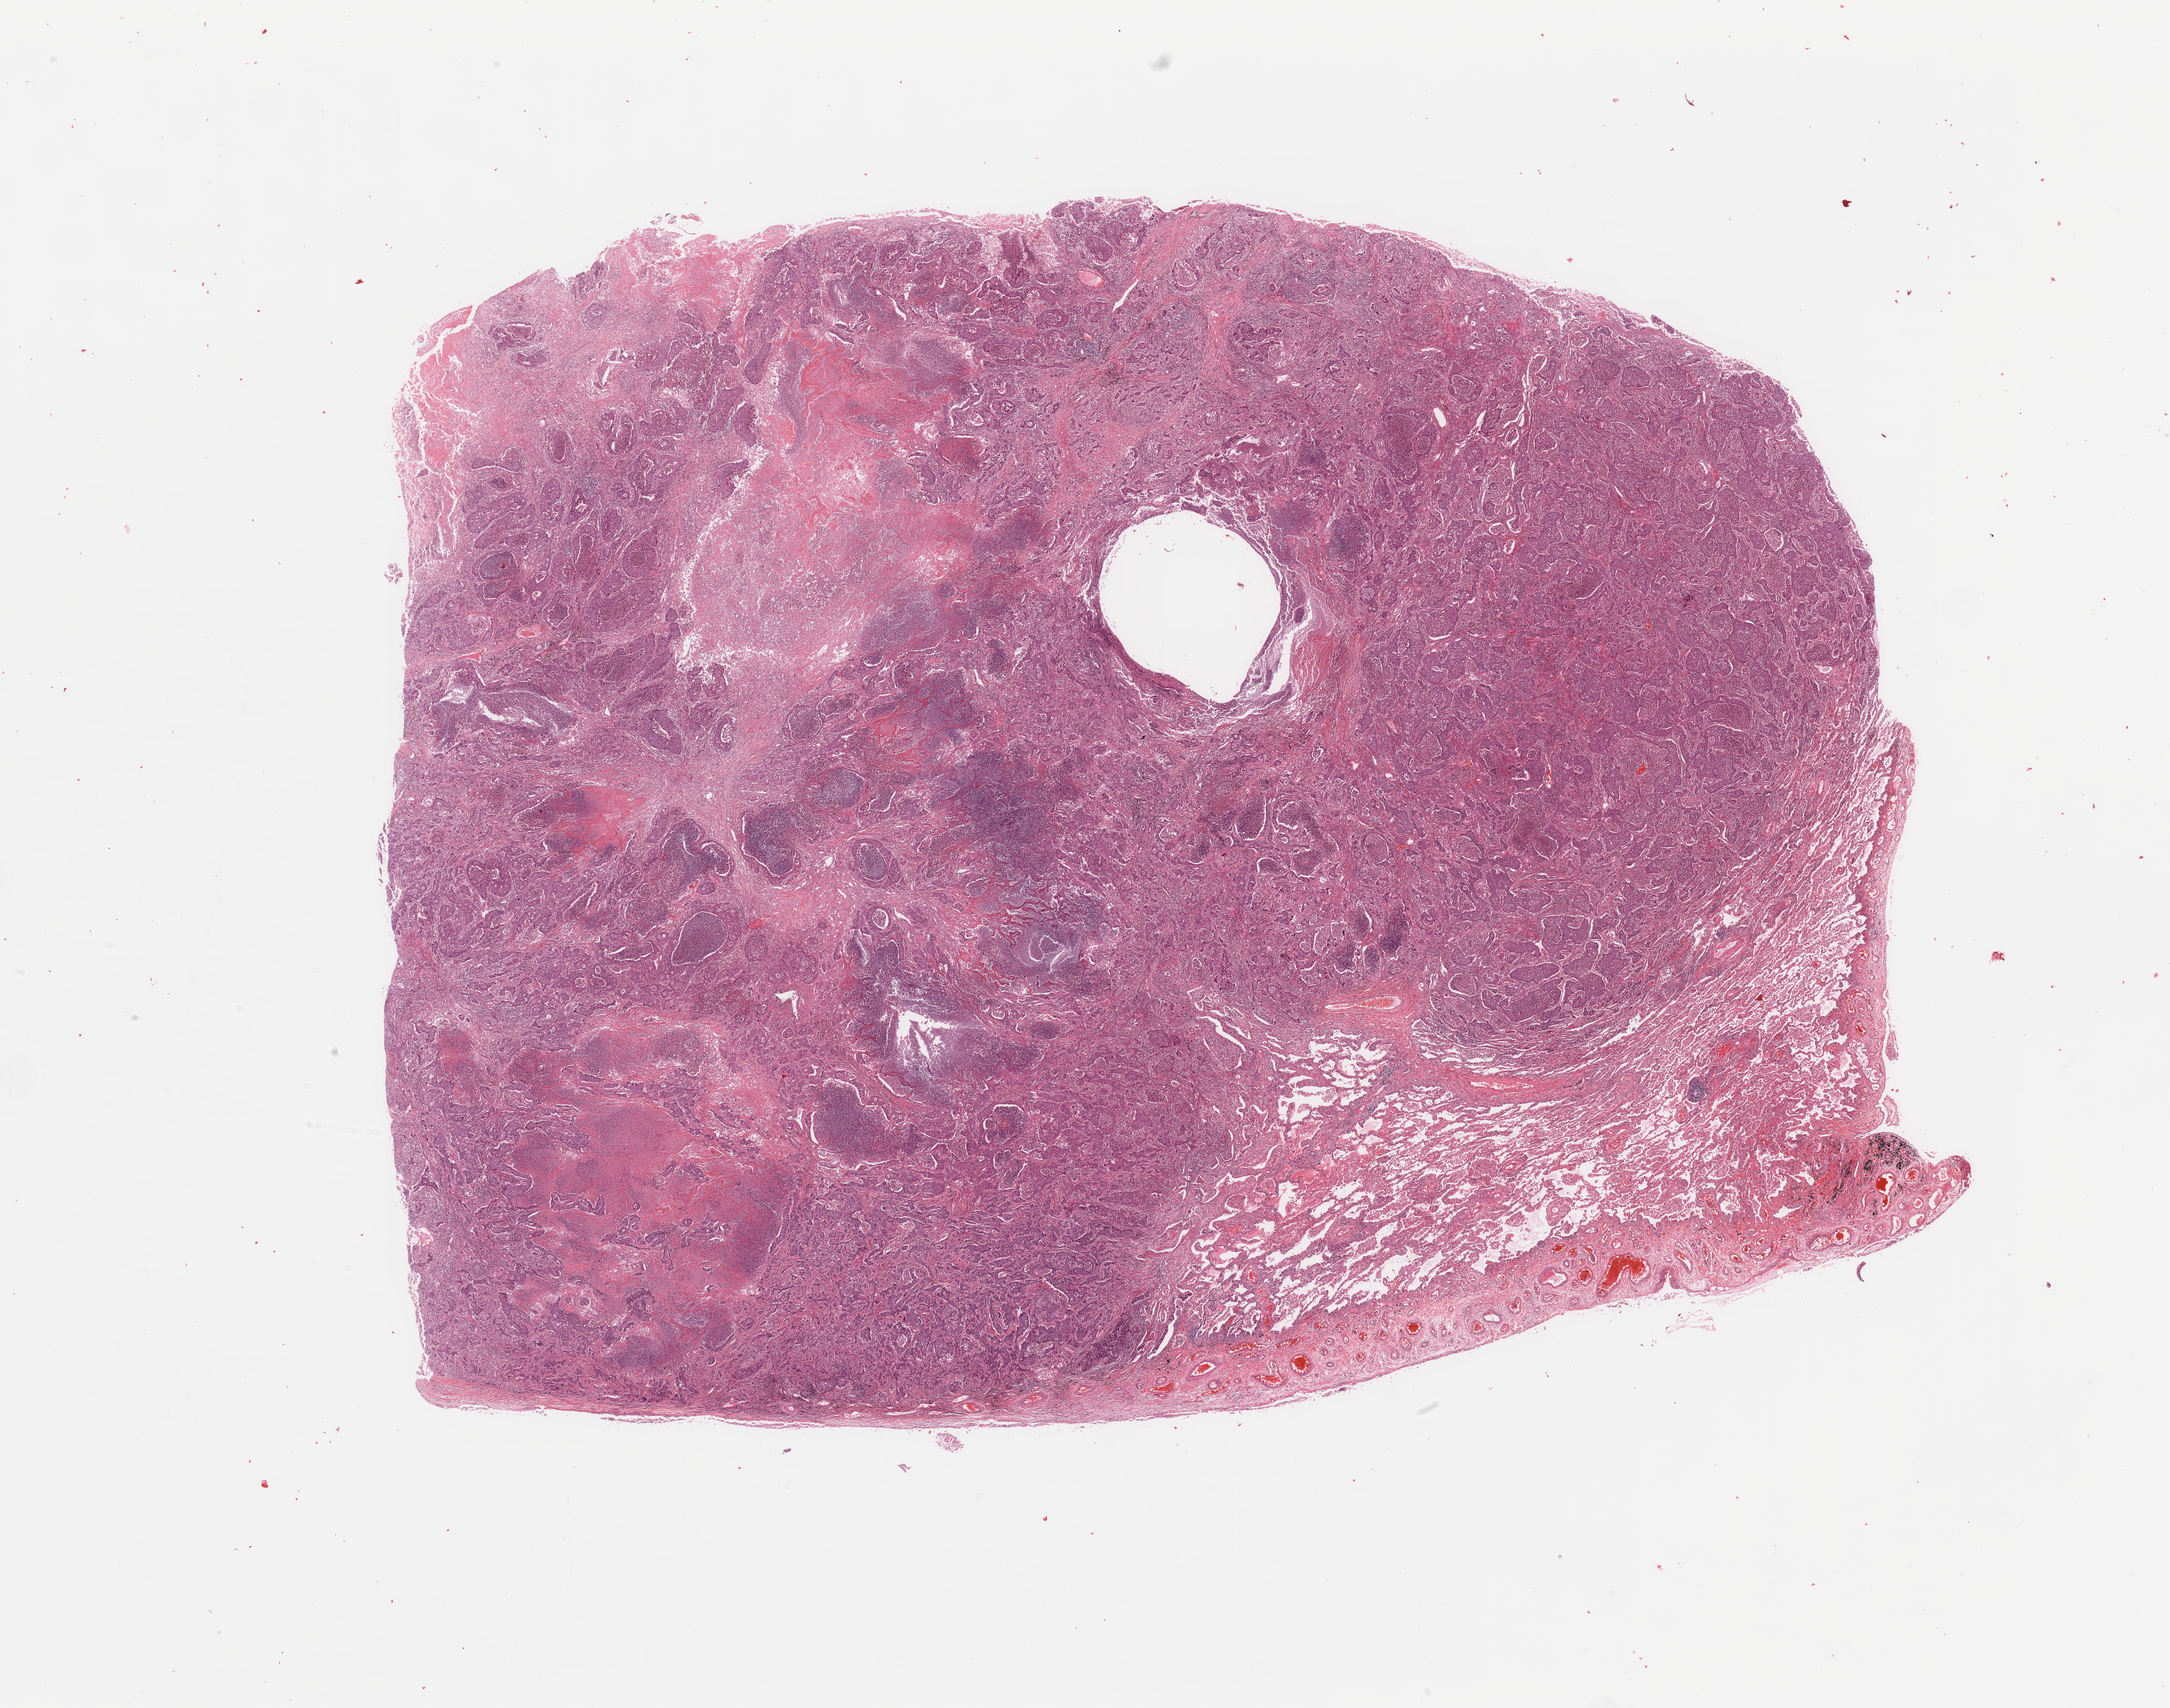
H&E whole-slide image — a low-resolution overview of the entire scanned area, about 27.6 x 21.7 mm (slide scanned at 20x); tumour tissue sample, lung. Patient: male, age 76 years. Histologic grade: G3 (poorly differentiated).
Histologic diagnosis: Adenocarcinoma, NOS. AJCC pathologic stage: IB.